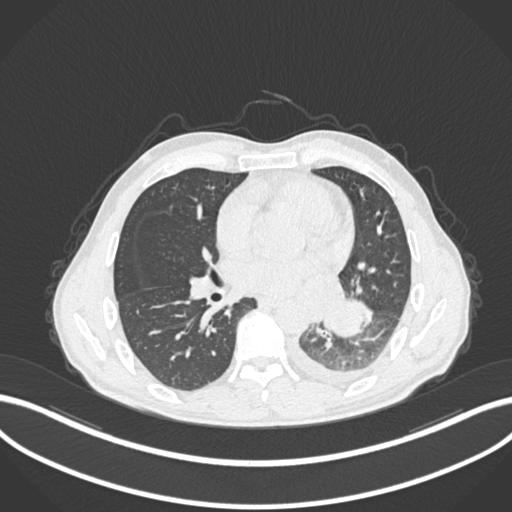
Chest CT, one axial slice; position 114 of 222 along the scan axis; reconstruction kernel B30f; lung window (W 1500 / L -600 HU); 1 mm slice thickness; 512 × 512 image matrix, field of view 400 × 400 mm. Male patient, age 47 years. Case-level facts recorded for this patient, not image findings: clinical TNM (as recorded): T3 N1 M1c; histopathological grade: G3.
Structures marked on this image (rectangle marked by the reading radiologist):
- lung tumour (recorded histology: small cell carcinoma): bounding box [x1, y1, x2, y2] px = [324, 298, 366, 339]